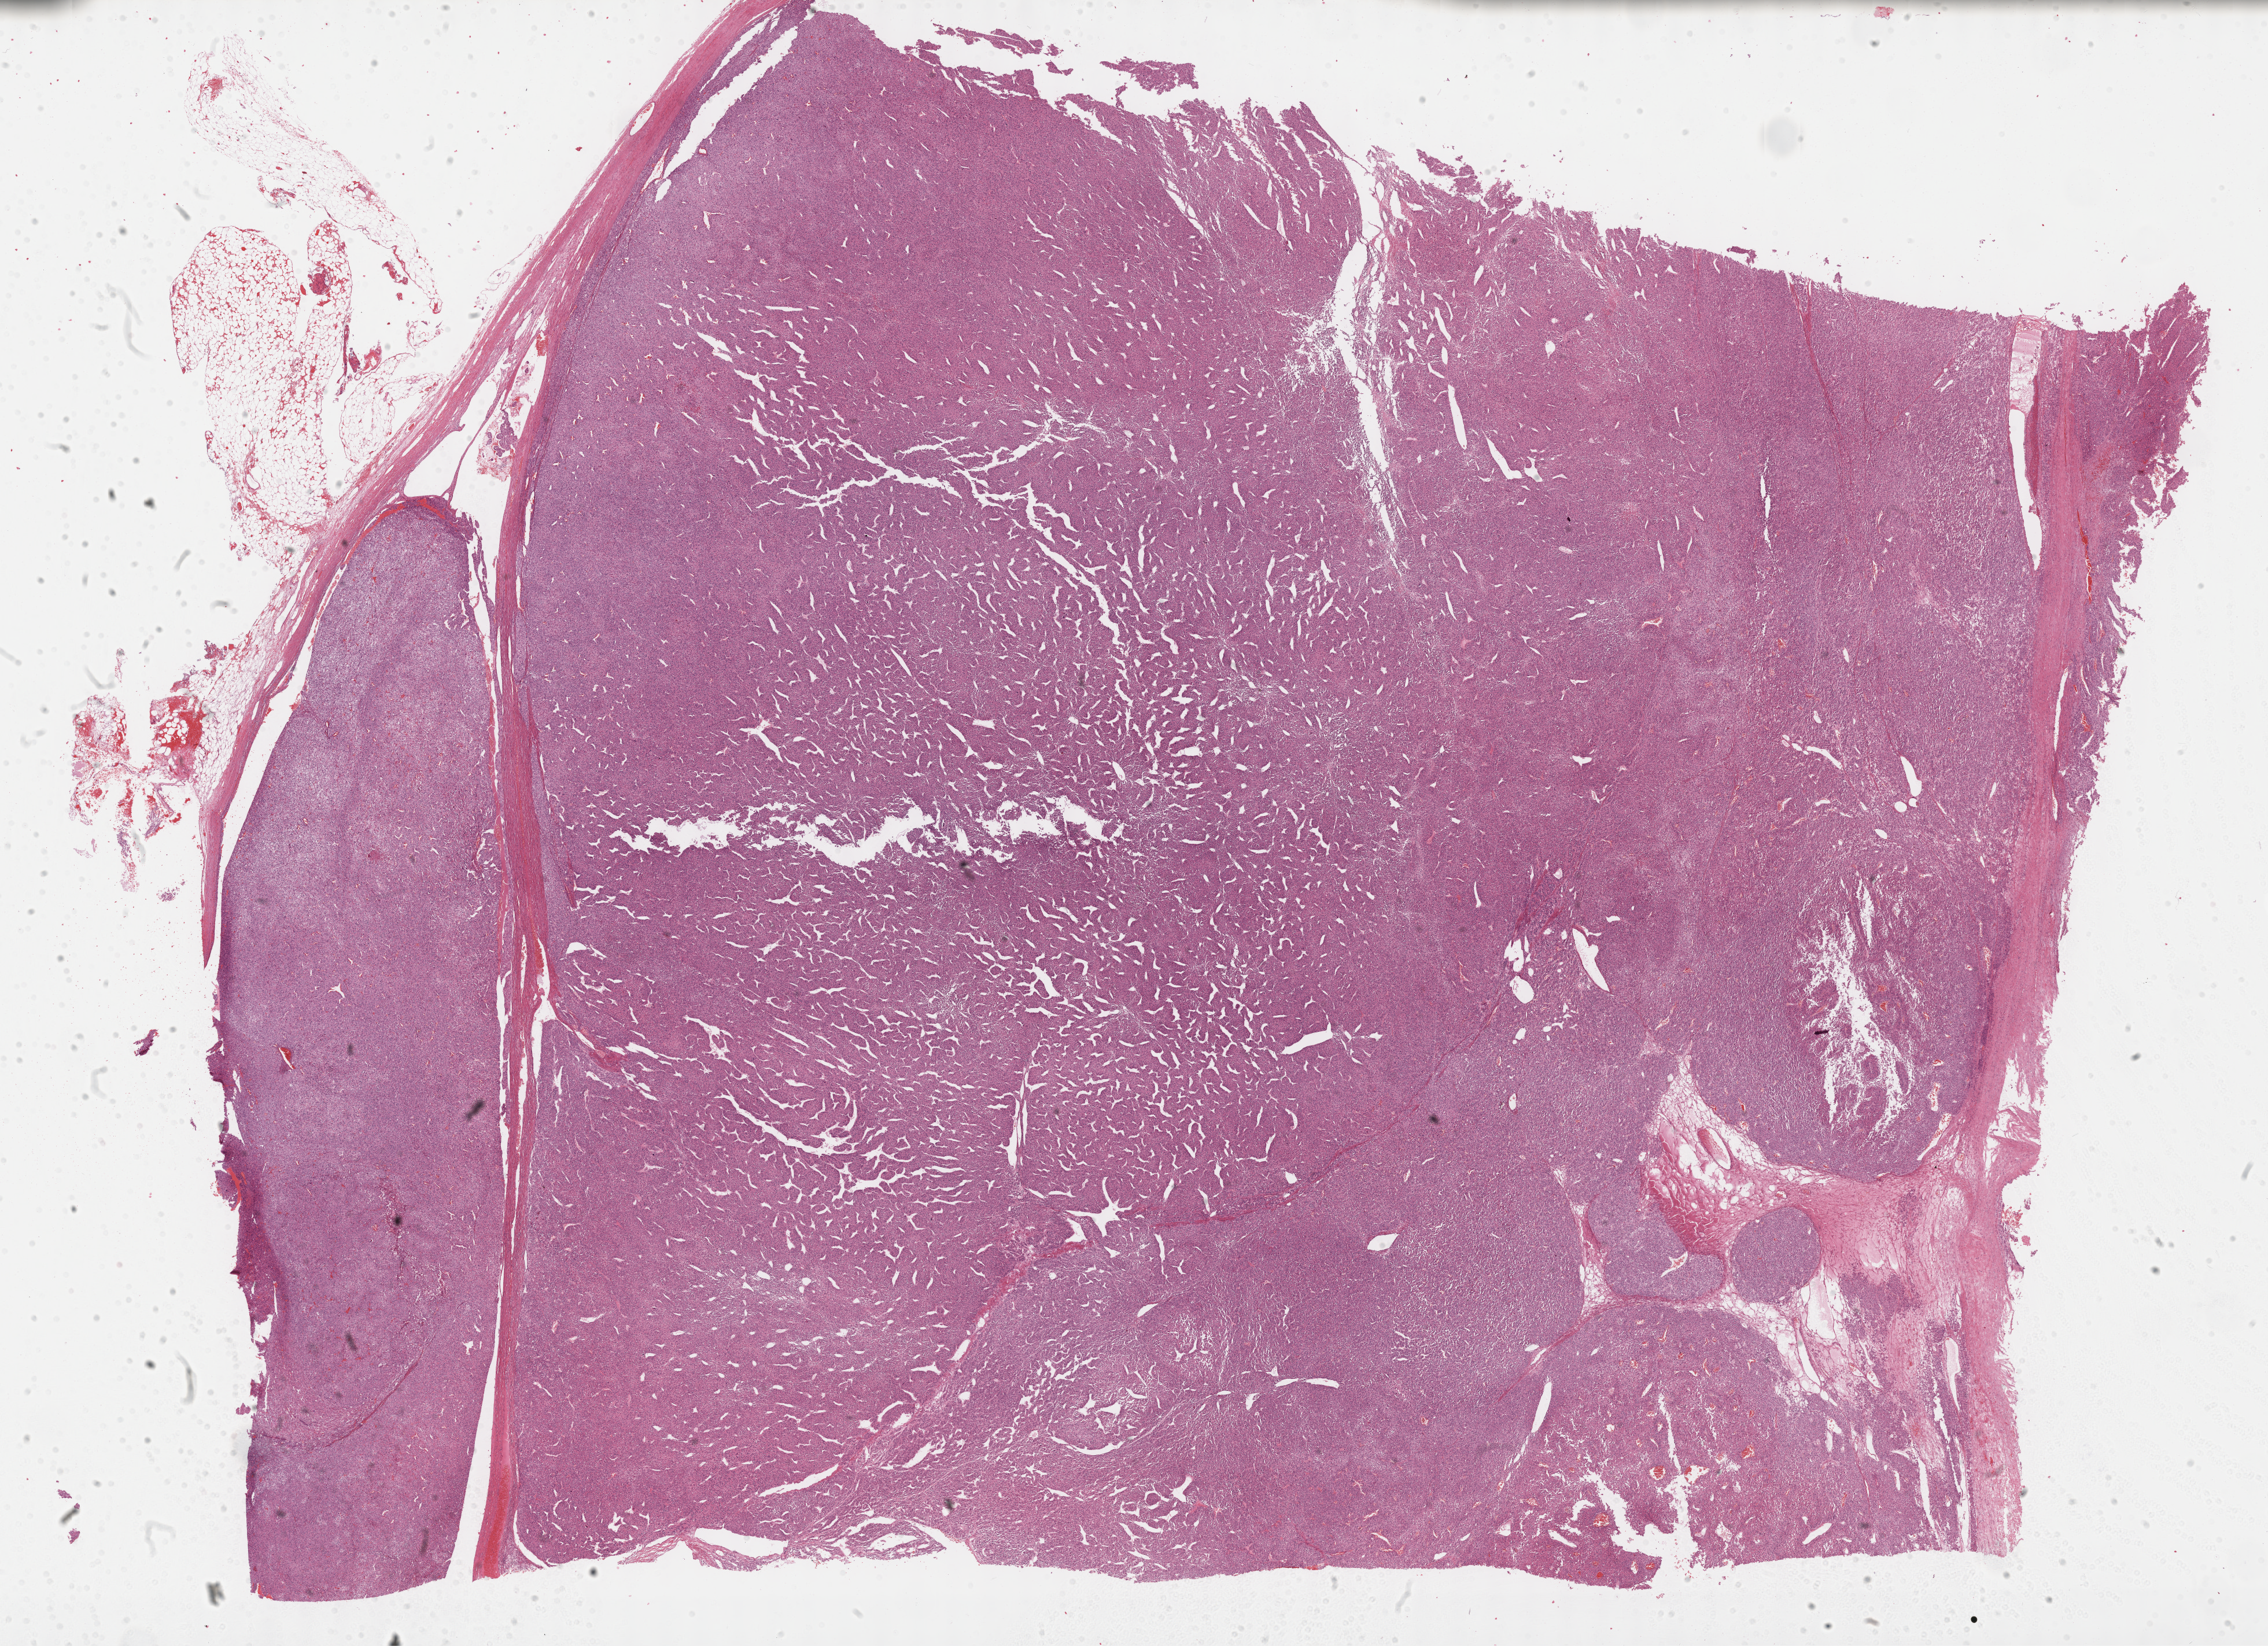
Hematoxylin and eosin (H&E) stained whole-slide image — shown as a low-resolution overview of the whole scanned area (about 31.7 x 23.0 mm, slide scanned at 40x); formalin-fixed paraffin-embedded (FFPE) diagnostic section; primary tumour sample from the adrenal cortex. Male patient; age at initial diagnosis 37 years.
Diagnosis: Adrenal cortical carcinoma (cortex of adrenal gland).